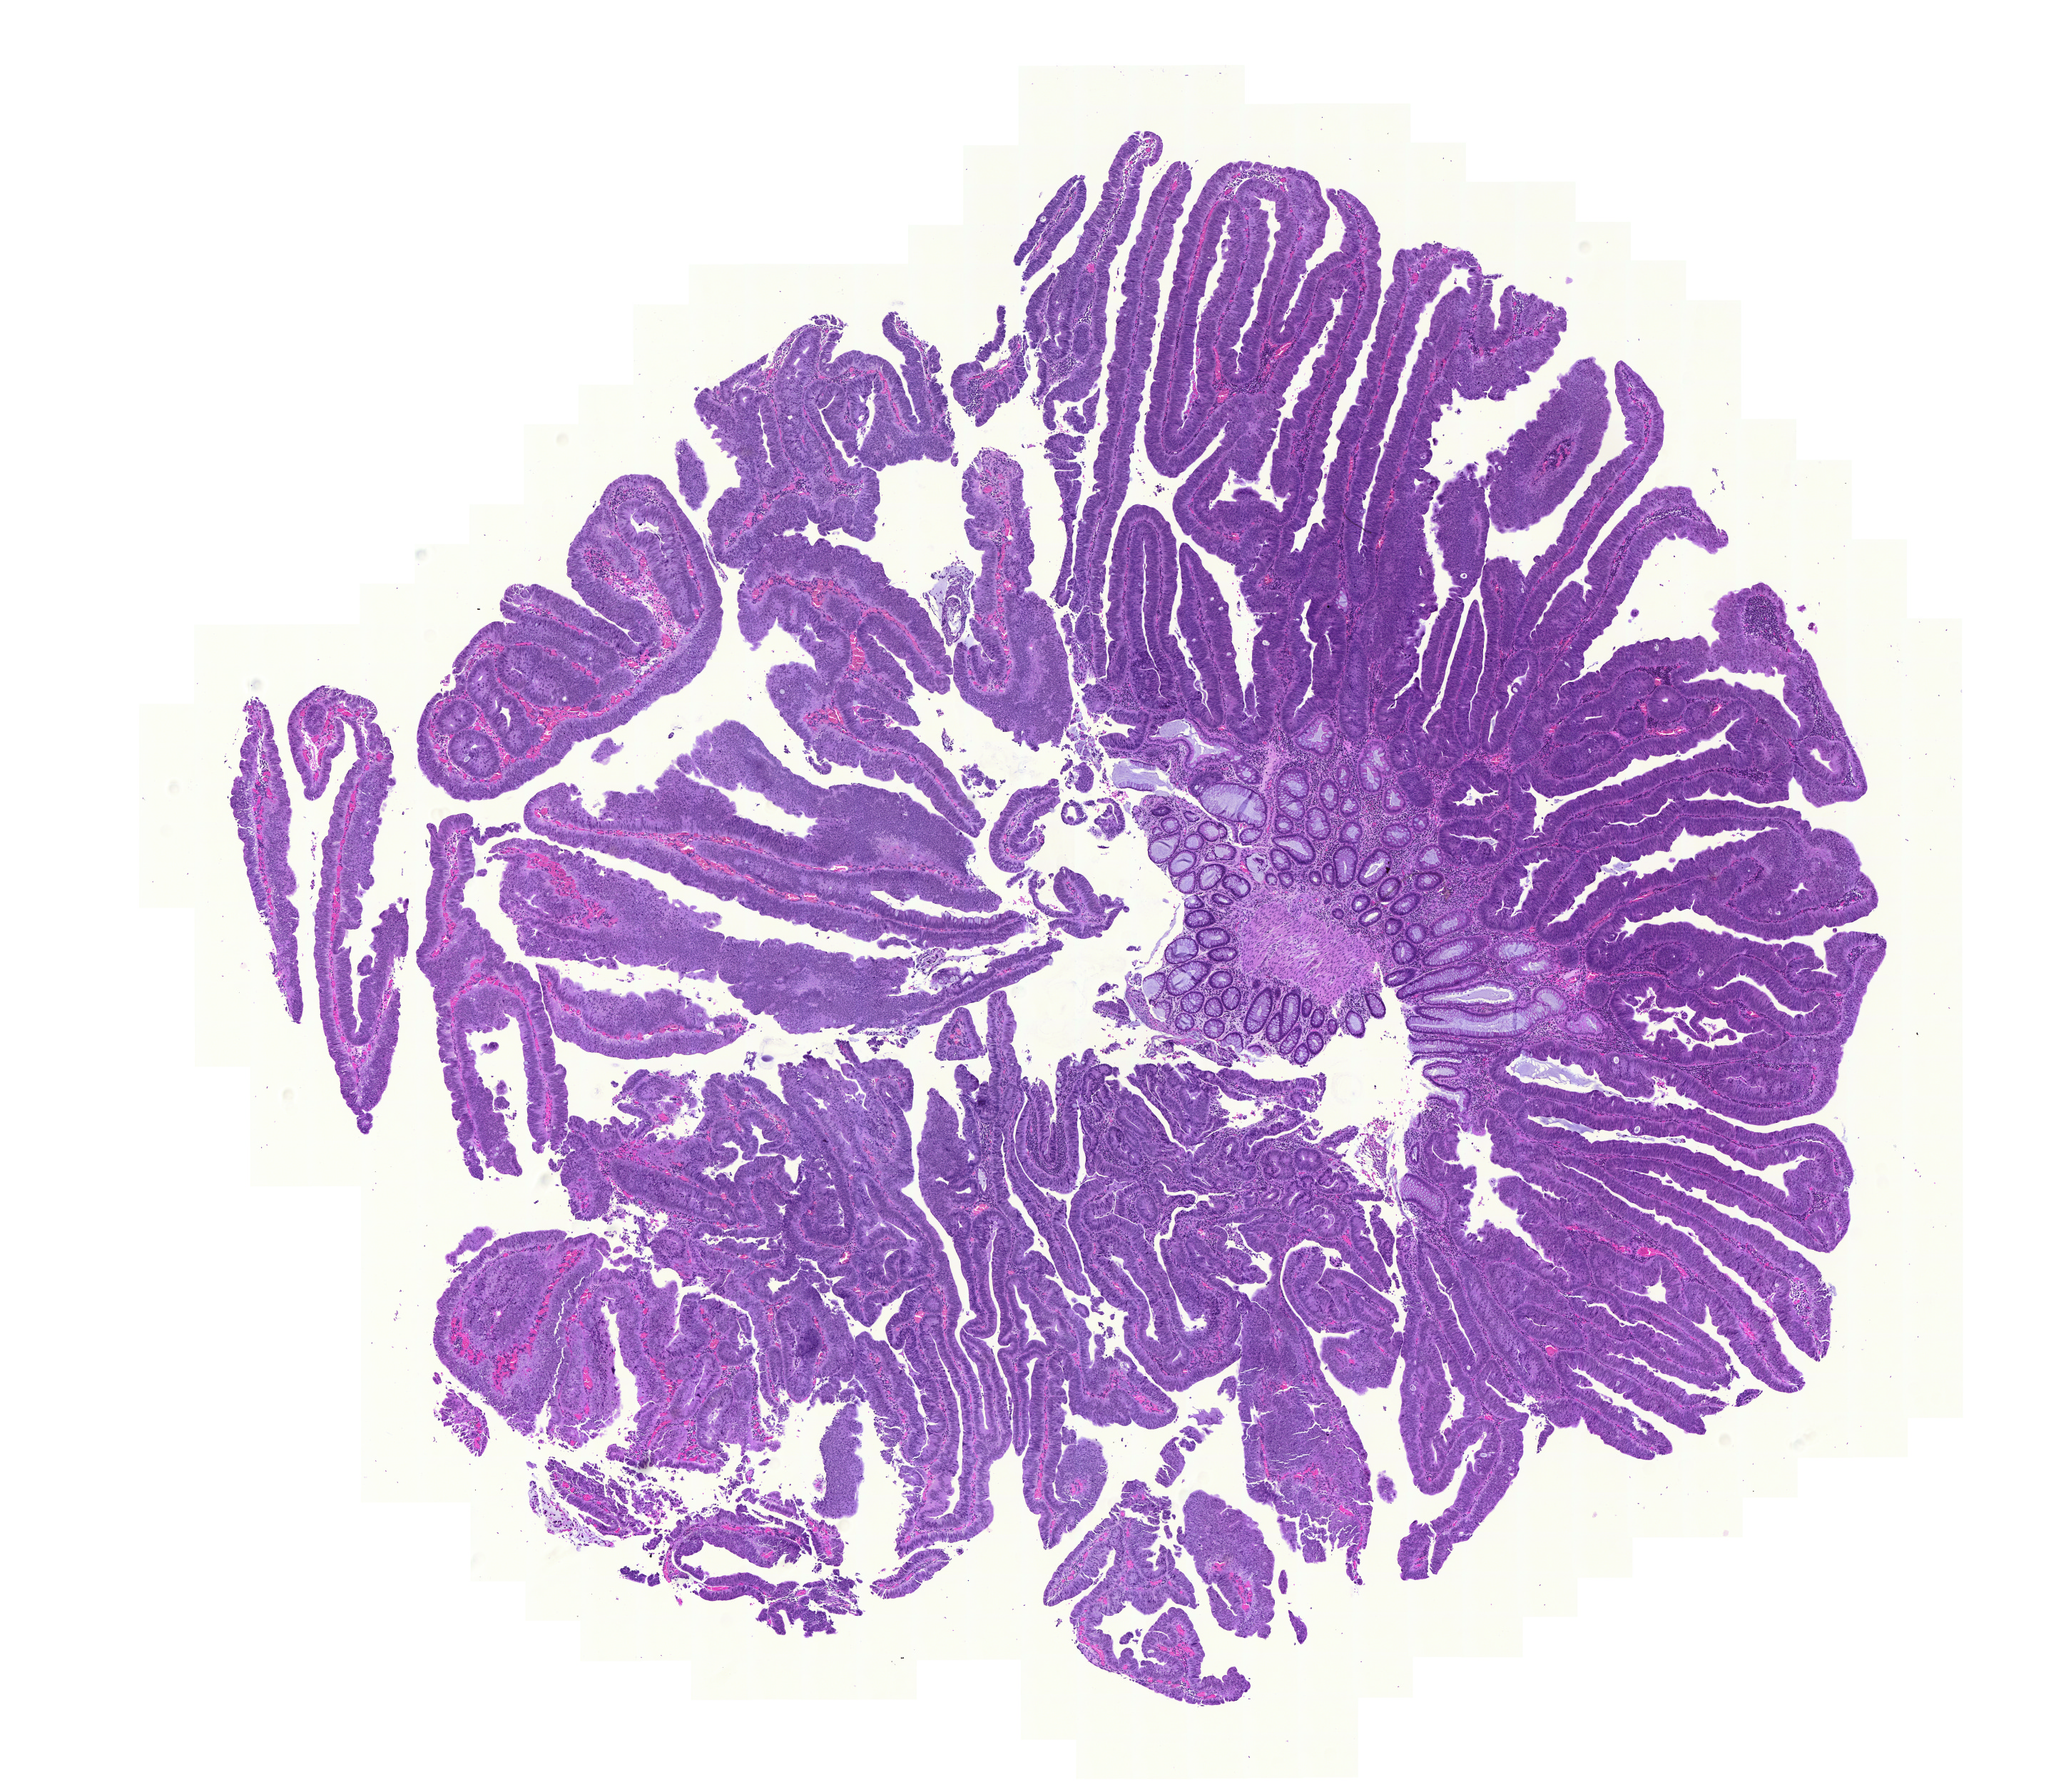
Hematoxylin and eosin (H&E) stained whole-slide image — whole scanned area (about 10.8 x 9.3 mm) shown as a low-resolution overview. Formalin-fixed paraffin-embedded (FFPE) diagnostic section. Sample: primary tumour, colon. Patient: male, age at initial diagnosis 80 years.
TNM: T1 N0 M0. Lymph nodes positive (case pathology): 0 of 17 examined. AJCC pathologic stage: I (6th edition). Diagnosis: Adenocarcinoma, NOS (sigmoid colon).